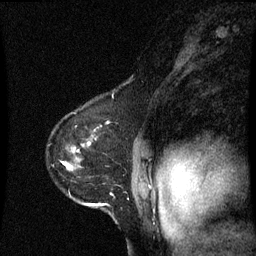
Breast MRI (dynamic contrast-enhanced), one sagittal slice. Slice 49 of 60 in the series (ordered by position). Dynamic contrast-enhanced series, image 2 of 3 at this slice position (ordered by acquisition). 1.5 T. TE 4.2 ms, TR 8.9 ms. 2 mm slice thickness. 256 × 256 image matrix, field of view 200 × 200 mm. Patient: female, 53 years. From the clinical record (not read from this slice): setting: breast cancer imaged before/during neoadjuvant chemotherapy; receptor status: HR-positive, HER2-negative.
Annotated regions visible in this slice (semi-automatically segmented with operator editing):
- analysis volume of interest (the breast-tissue region the enhancement analysis was run in; not a lesion): bounding box <62,110,145,219> (left, top, right, bottom; pixels)
- tumour enhancement mask (voxels above the 70 % enhancement threshold inside the analysis volume of interest): <62,150,91,207>